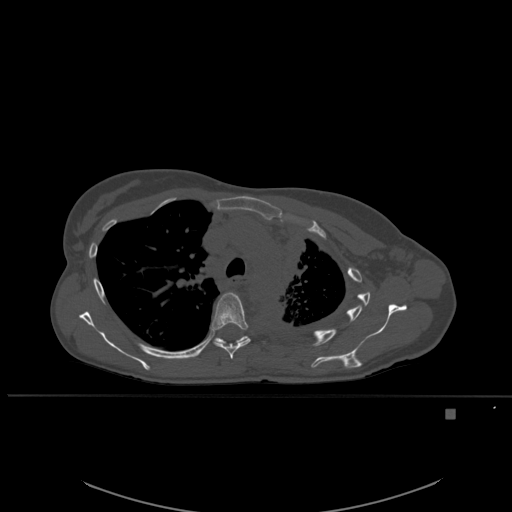
CT including the spine, one axial slice. Position 396 of 537 along the scan axis. Bone window (W 1800 / L 400 HU). 512 × 512 image matrix, field of view 440 × 440 mm. Female patient, age 45 years. From the clinical record (not read from this slice): primary cancer: lung.
Outlined on this slice (semi-automatically segmented with operator editing):
- T5 vertebra: bounding box (x1, y1, x2, y2) in pixels: (210, 292, 251, 360)
- T6 vertebra: (214, 336, 249, 344)